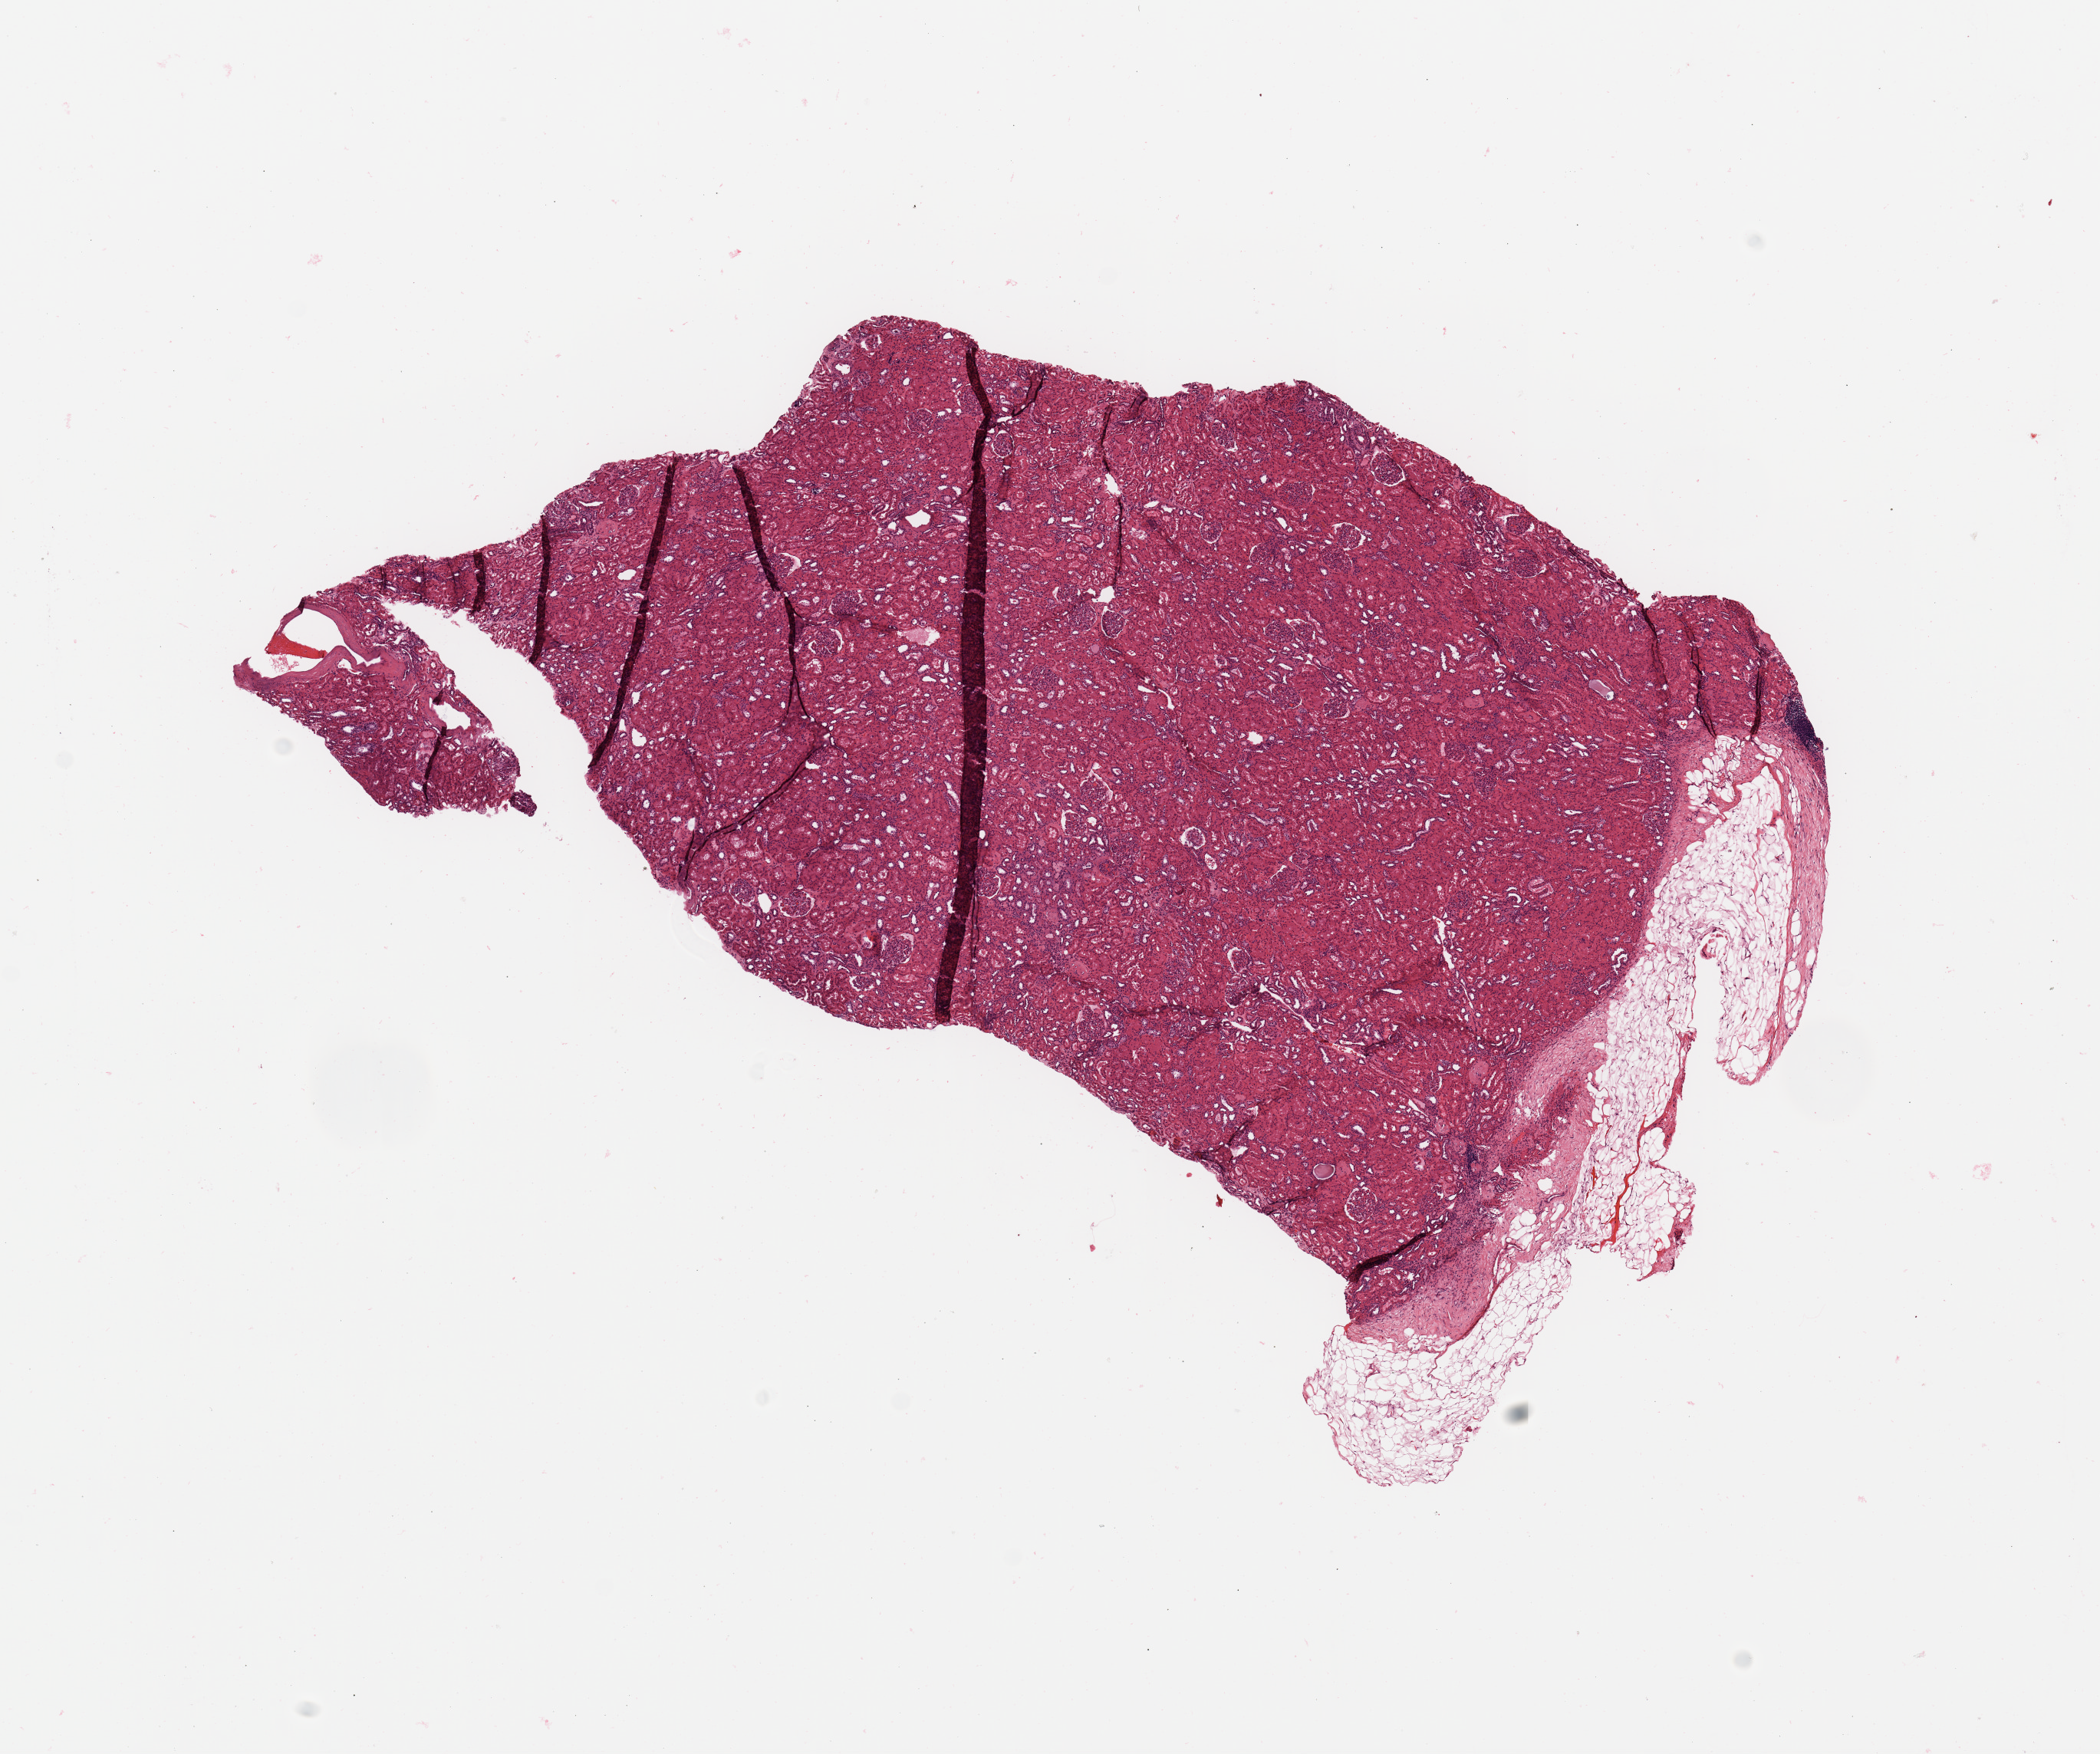
Digitized Hematoxylin and eosin (H&E) stained tissue section (whole slide), a low-resolution overview of the entire scanned area, about 10.8 x 9.0 mm, normal (non-tumour) tissue sample, kidney. Female, 64 y/o.
* this section: normal (non-tumour) tissue from the same patient
* patient diagnosis: Renal cell carcinoma, NOS